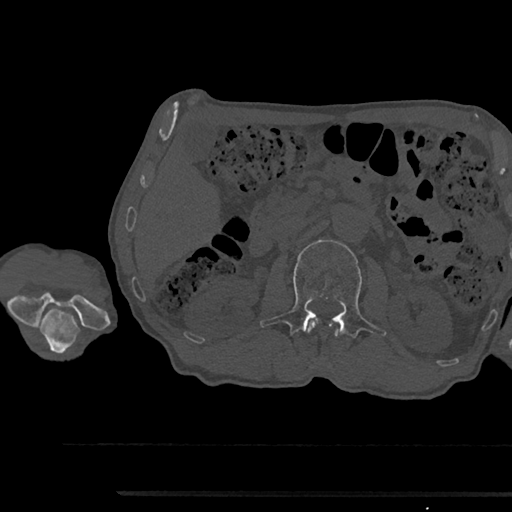
CT including the spine, one axial slice; position 578 of 797 along the scan axis; reconstruction kernel Br40s/3; 120 kVp; bone window (W 1800 / L 400 HU); 0.5 mm slice thickness; 512 × 512 image matrix, field of view 367 × 367 mm. Patient: male, 79 years. Case-level facts recorded for this patient, not image findings: primary cancer: prostate.
Outlined on this slice (semi-automatically segmented with operator editing):
- L1 vertebra: bounding box [x1, y1, x2, y2] px = [308, 320, 340, 338]
- L2 vertebra: [260, 240, 386, 361]